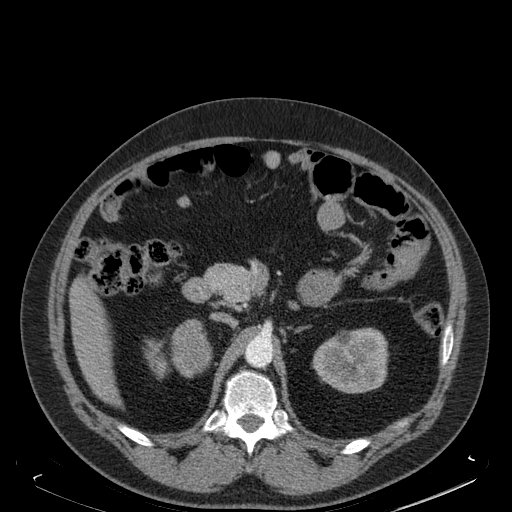
Contrast-enhanced abdominal CT, one axial slice. Slice 104 of 181 in the series (ordered by position). Soft-tissue window (W 400 / L 40 HU). 1.5 mm slice thickness. 512 × 512 image matrix, field of view 405 × 405 mm. Male patient. Case-level facts recorded for this patient, not image findings: diagnosis: adrenocortical carcinoma; tumour side: right adrenal; tumour size at pathology: 7.5 cm.
Structures marked on this image (semi-automatically segmented with operator editing):
- mass: bounding box (x1, y1, x2, y2) in pixels: (173, 319, 210, 376)